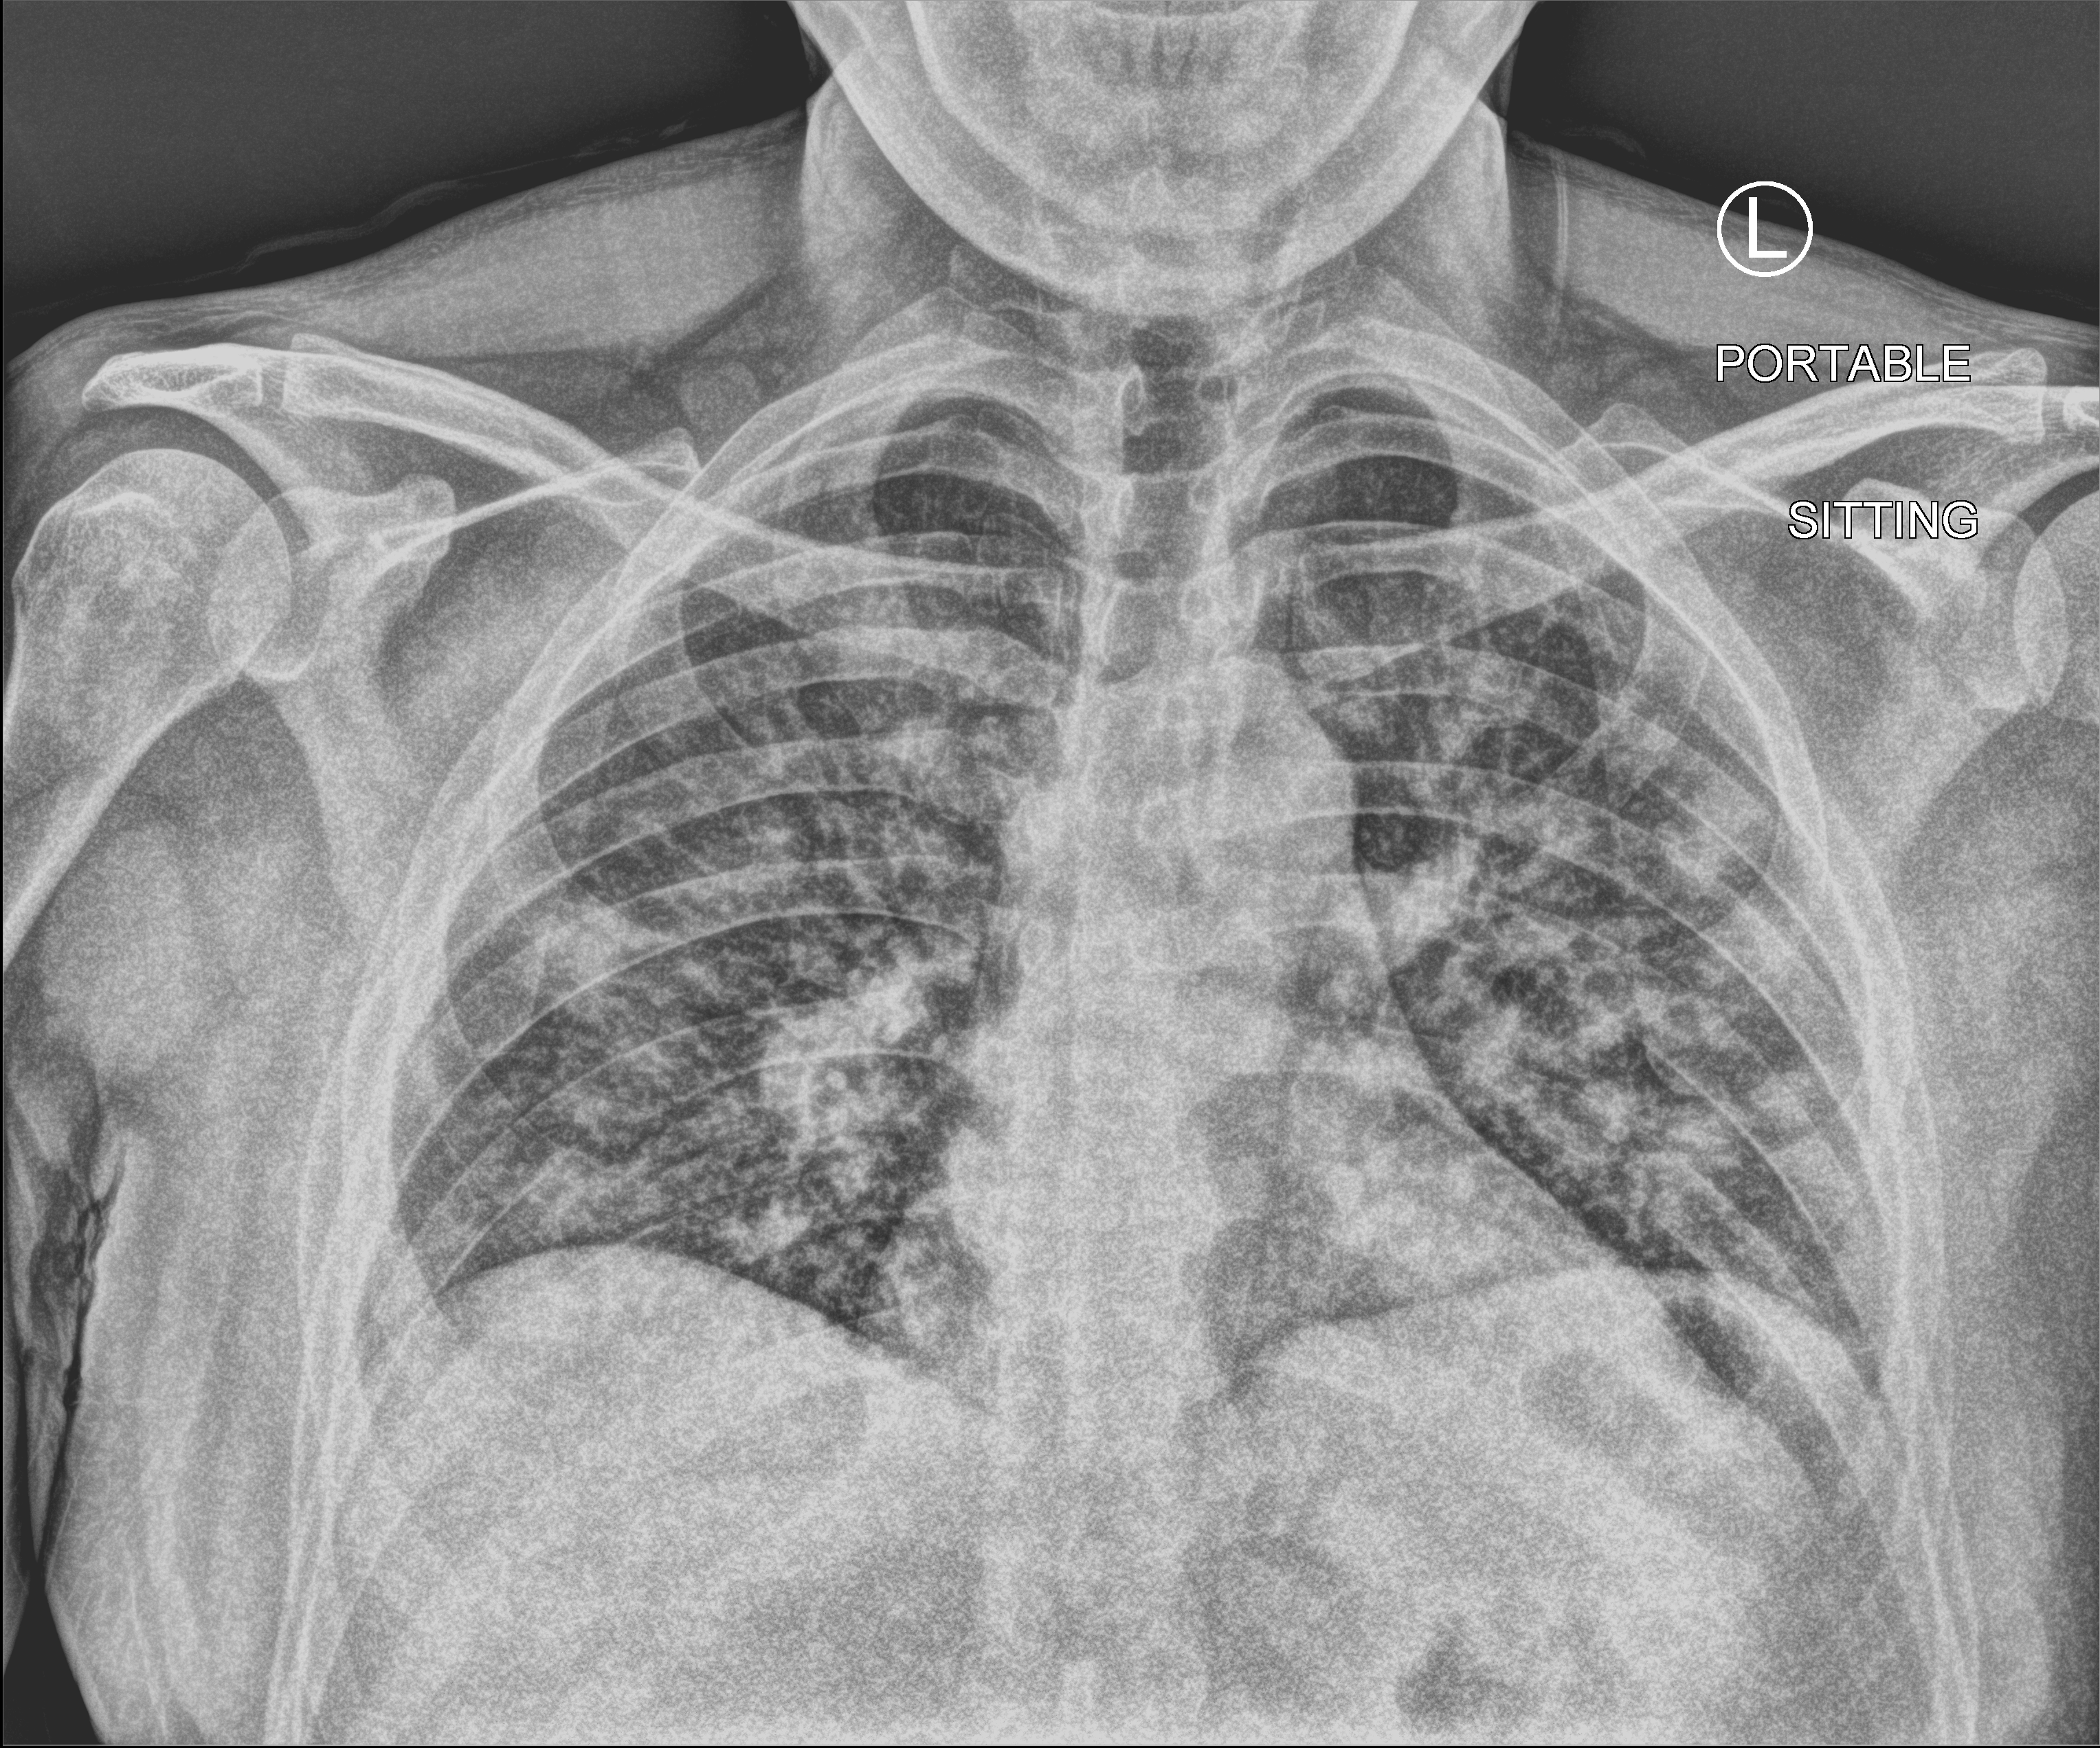
Bedside chest radiograph (computed radiography). Patient hospitalised with COVID-19; male, aged 18–59 years.
Hospital-stay facts (about this admission, not read from this image; timing relative to this image not recorded):
- mechanically ventilated during this hospital stay: no
- admitted to intensive care during this hospital stay: no